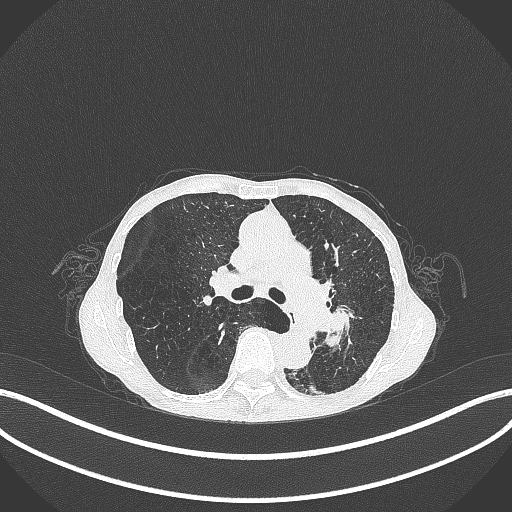
Chest CT, one axial slice. Slice 174 of 347 in the series (ordered by position). Lung window (W 1500 / L -600 HU). 1 mm slice thickness. 512 × 512 image matrix, field of view 400 × 400 mm. Patient: female, 70 years. From the clinical record (not read from this slice): clinical TNM (as recorded): T3 N0 M0; histopathological grade: G3.
Outlined on this slice (rectangle marked by the reading radiologist):
- lung tumour (recorded histology: small cell carcinoma): box from (x=316, y=302) to (x=355, y=350) px